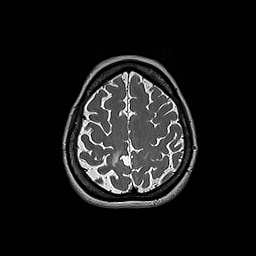
Brain MRI from a brain-tumour surgery series, one axial slice; position 52 of 192 along the scan axis; 256 × 256 image matrix, field of view 250 × 250 mm. From the clinical record (not read from this slice): histopathology: Oligodendroglioma; WHO grade: 2; IDH mutation: yes; tumour location: Right Parietal.
Structures marked on this image (manually delineated by an expert):
- tumour: box from (x=111, y=150) to (x=121, y=169) px